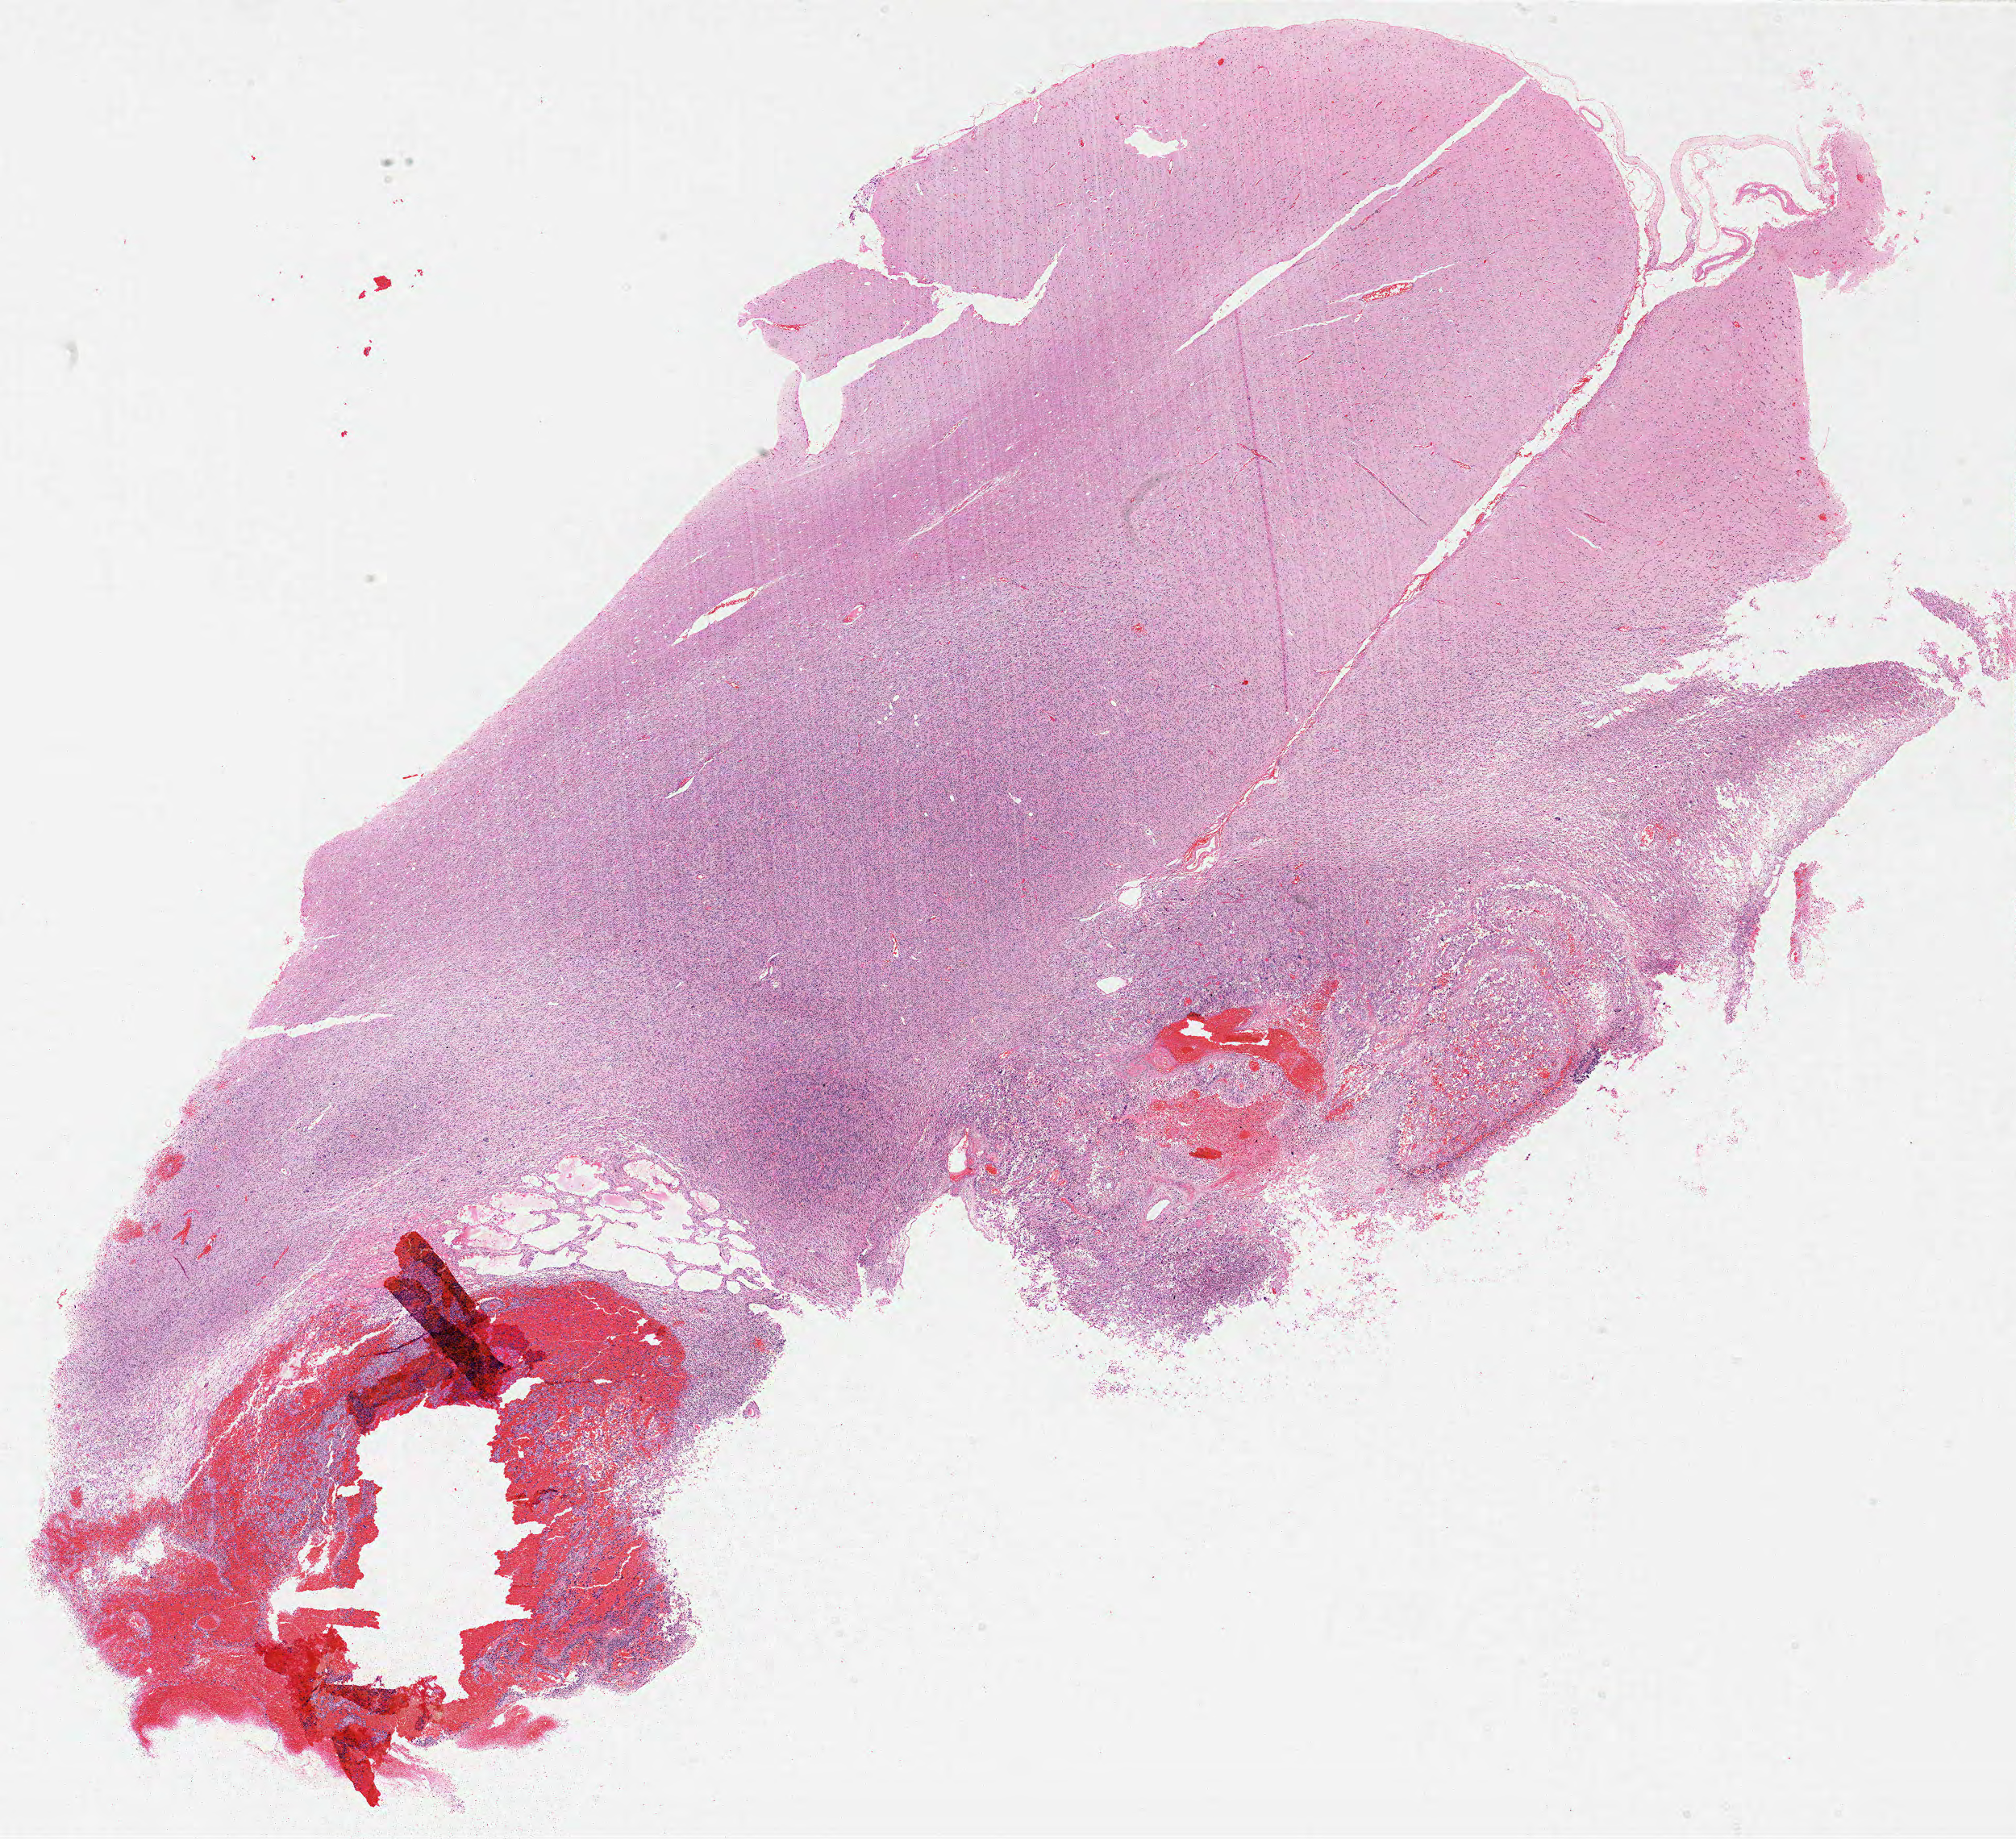
Hematoxylin and eosin (H&E) stained whole-slide image — low-resolution overview of the scanned area, about 20.0 x 18.2 mm. Formalin-fixed paraffin-embedded (FFPE) diagnostic section. Brain, primary tumour sample. Male, age 51 years at initial diagnosis.
Diagnosis: Glioblastoma.